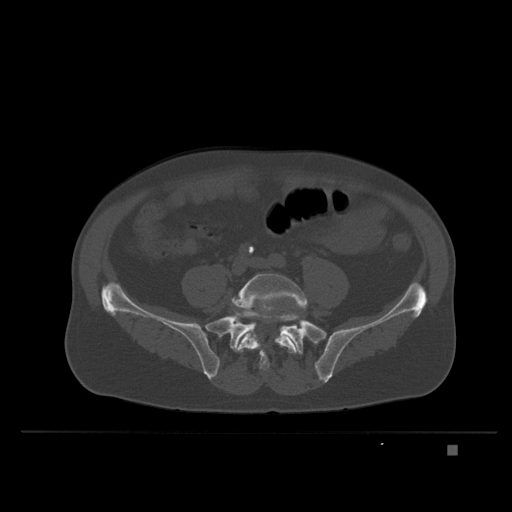
CT including the spine, one axial slice; position 50 of 435 along the scan axis; bone window (W 1800 / L 400 HU); 512 × 512 image matrix, field of view 434 × 434 mm. Patient: male, 73 years. Case-level facts recorded for this patient, not image findings: primary cancer: skin.
Outlined on this slice (semi-automatic segmentation, software-assisted and operator-edited):
- L5 vertebra: box from (x=232, y=273) to (x=307, y=371) px